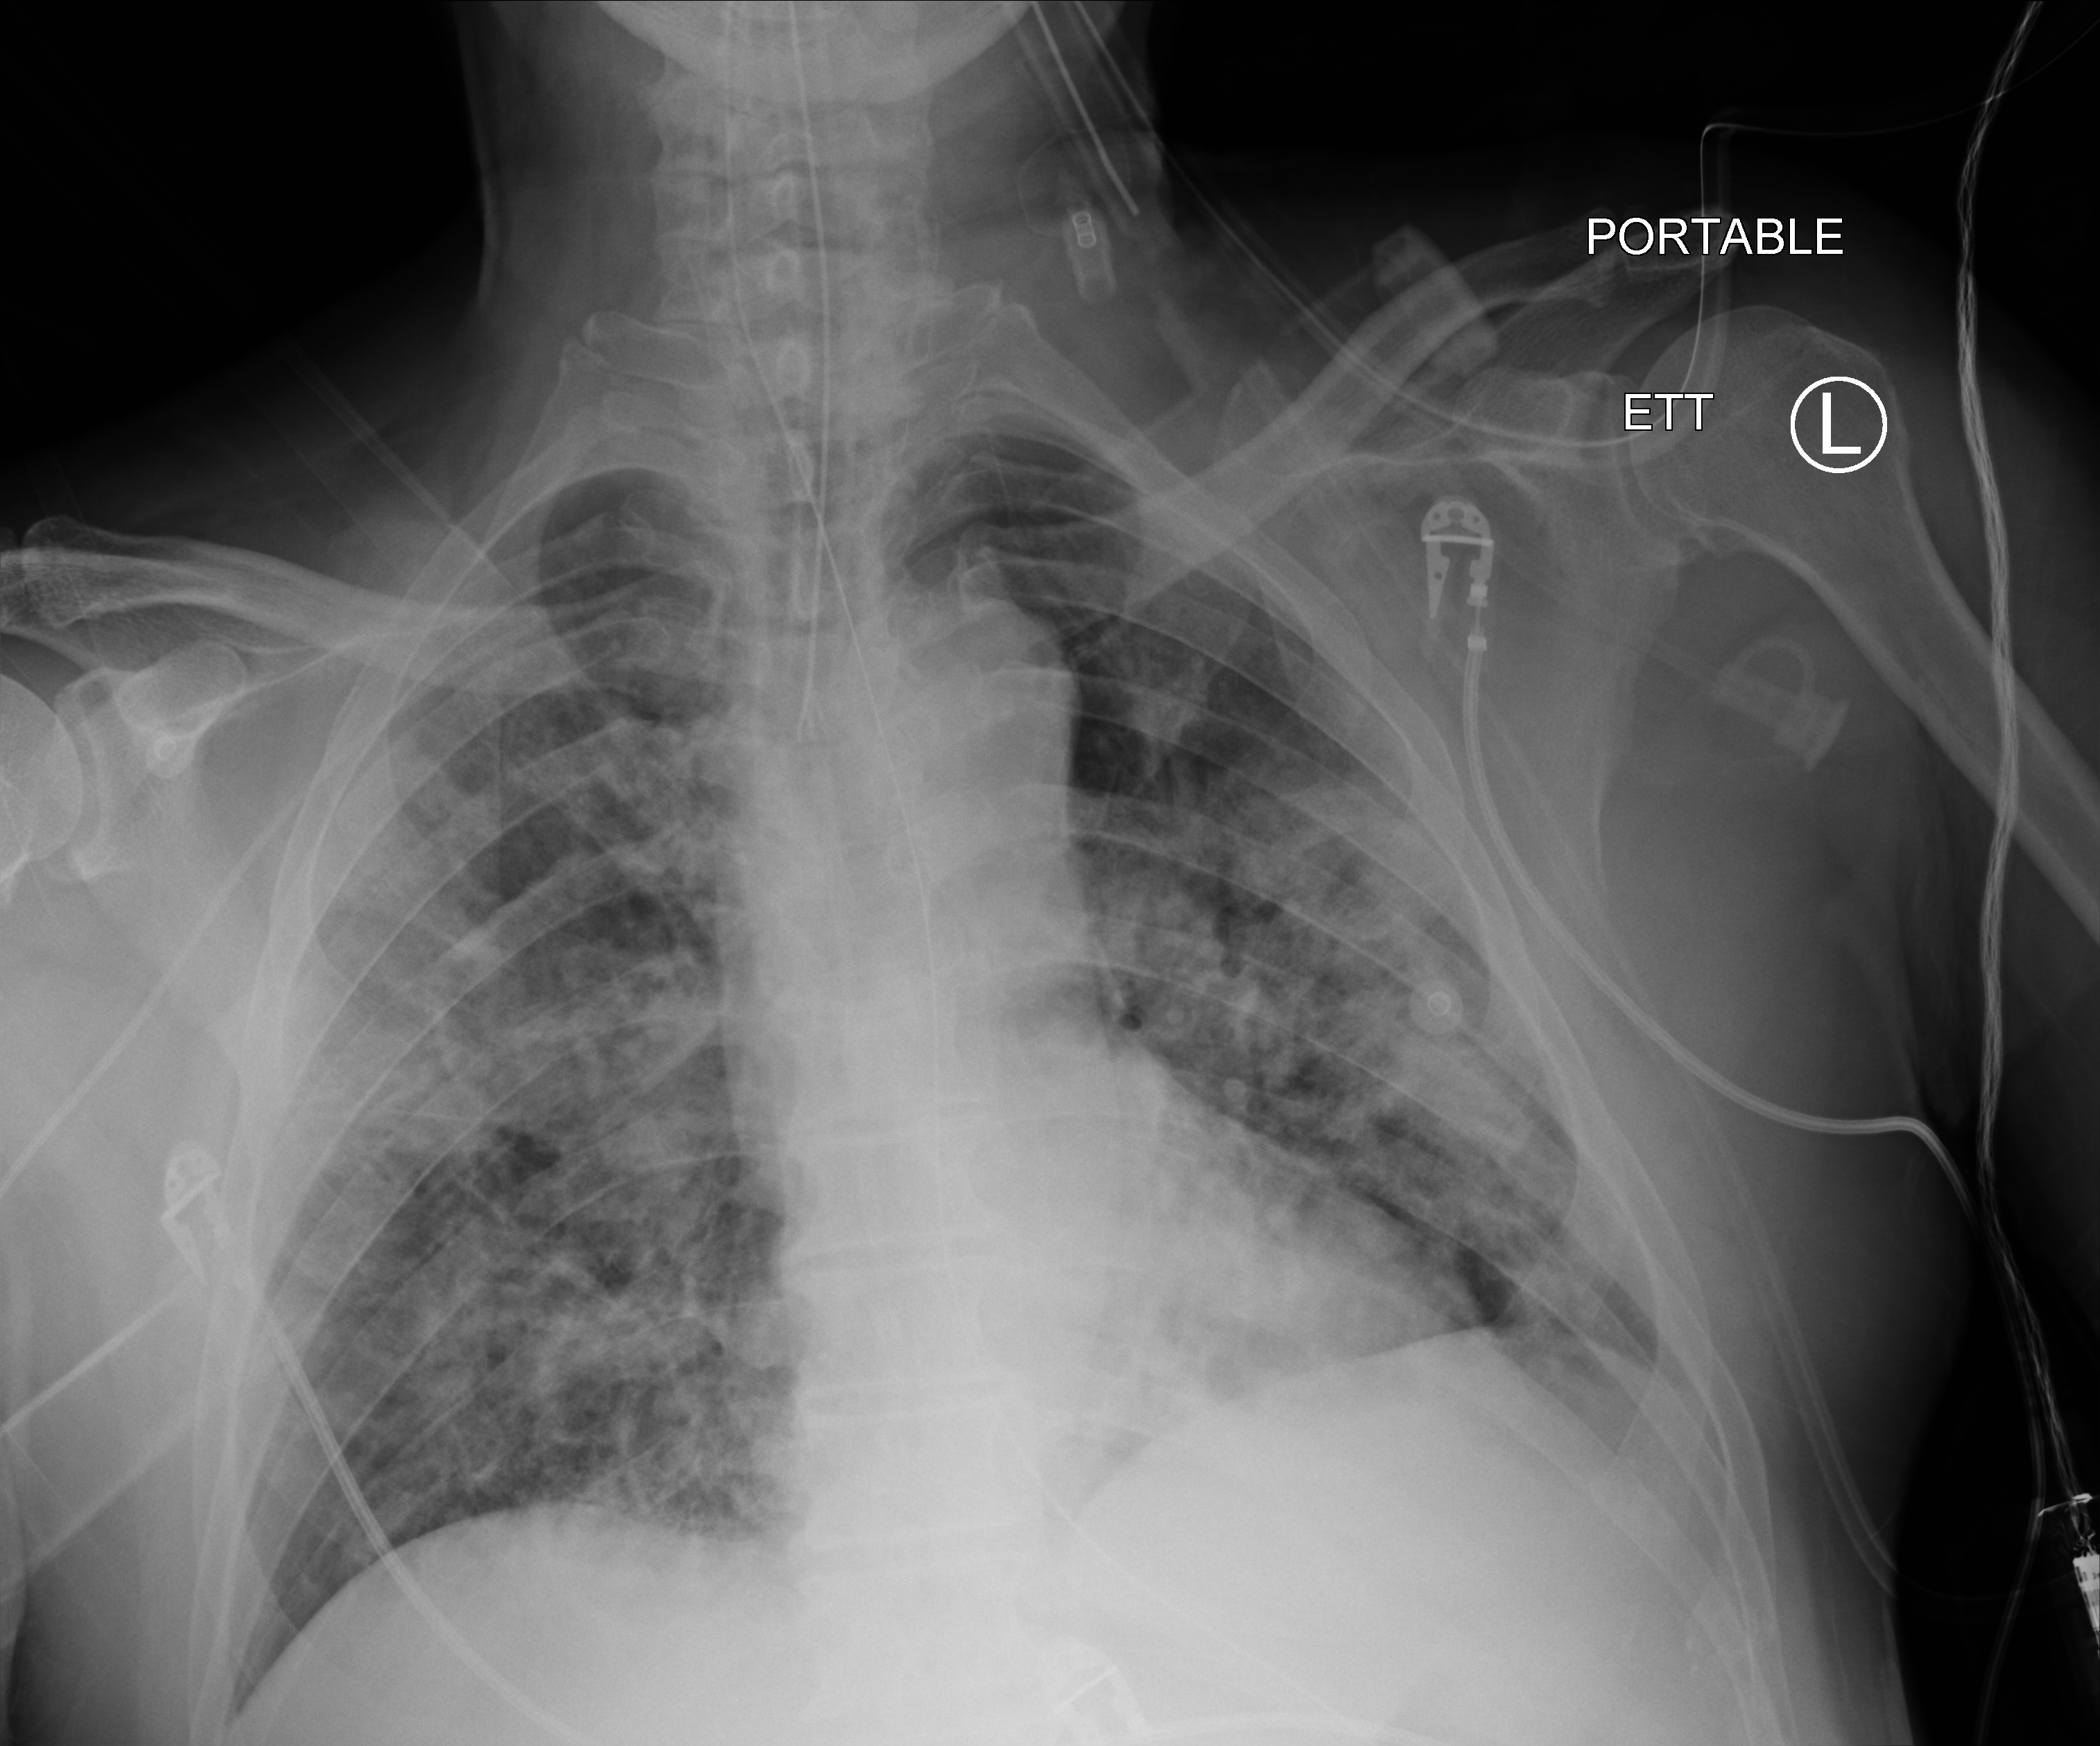
Chest X-ray (portable); anteroposterior (AP) projection. Patient hospitalised with COVID-19; male, aged 60–74 years.
From the hospital-stay record, not from the radiograph (when in the stay this image was taken is not recorded): length of hospital stay: 20 days.